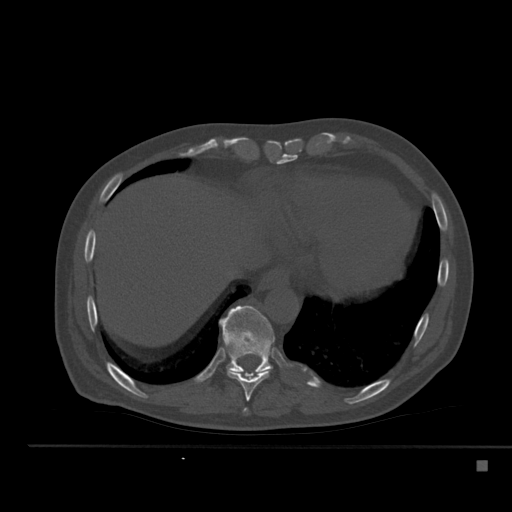
CT including the spine, one axial slice. Position 280 of 517 along the scan axis. Reconstruction kernel Br40s. Bone window (W 1800 / L 400 HU). 1.5 mm slice thickness. 512 × 512 image matrix, field of view 408 × 408 mm. Patient: male, 70 years. From the clinical record (not read from this slice): primary cancer: renal.
Outlined on this slice (semi-automatically segmented with operator editing):
- T10 vertebra: bounding box [x1, y1, x2, y2] px = [219, 305, 275, 376]
- T8 vertebra: [243, 409, 249, 413]
- T9 vertebra: [222, 347, 270, 401]